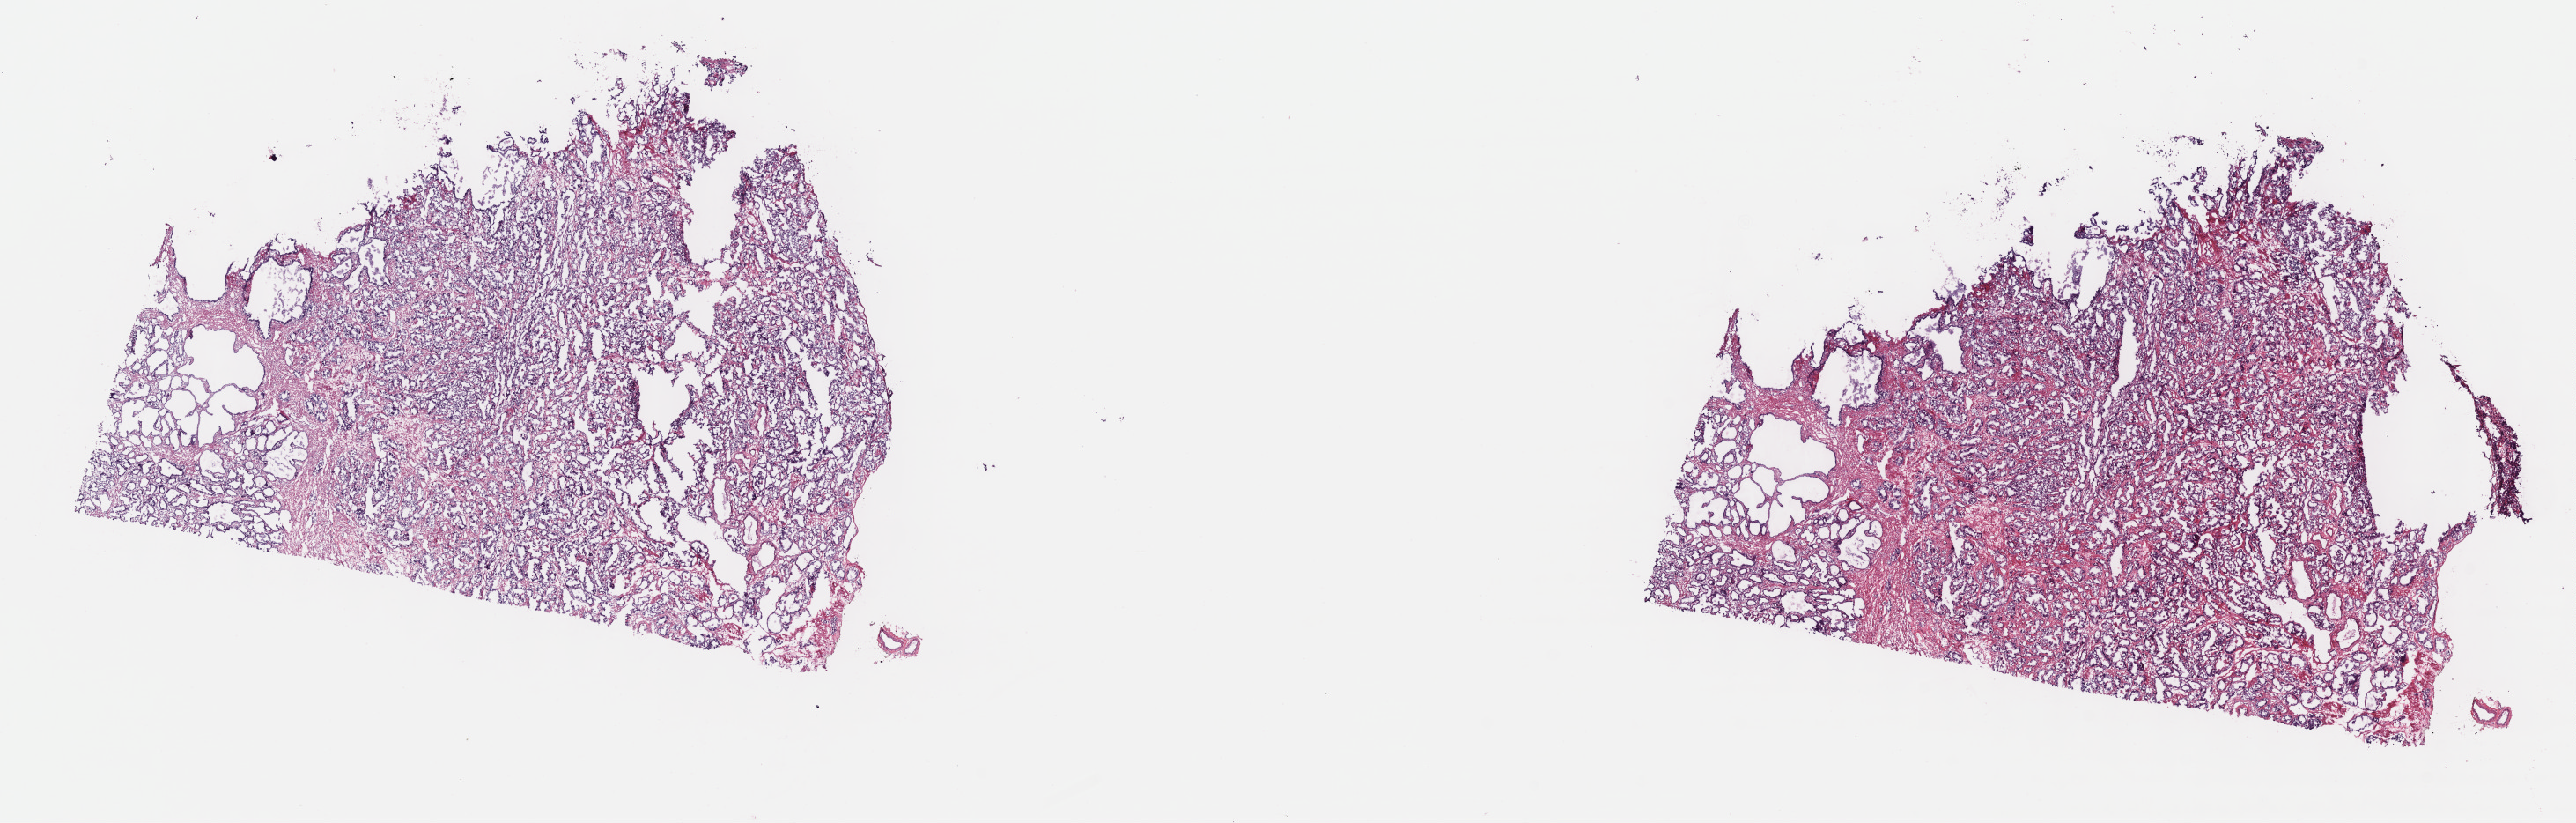
Whole-slide histology image, H&E-stained, a low-resolution overview of the entire scanned area, about 23.7 x 7.6 mm (acquisition: 40x scan). Frozen section. Primary tumour sample from the prostate. Patient: male, age at initial diagnosis 63 years. Gleason score: 7 (3+4). Pathologist review of this section (percent, as recorded): tumour cells 85%, tumour nuclei 75%, normal cells 15%, stromal cells 0%, necrosis 0%. Infiltration values recorded for this section: lymphocyte infiltration 0%, monocyte infiltration 0%, neutrophil infiltration 0%.
Diagnosis: Adenocarcinoma, NOS (prostate gland).